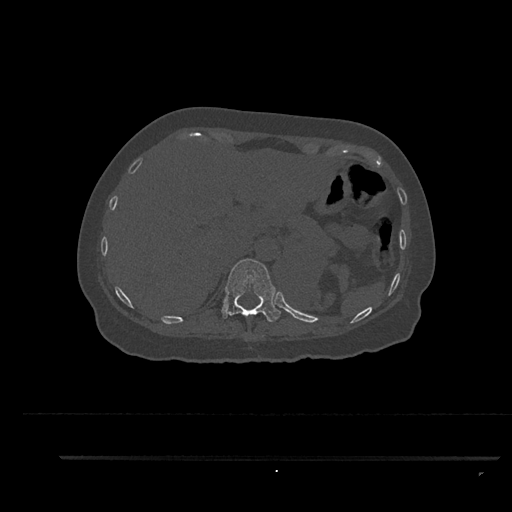
CT including the spine, one axial slice; position 320 of 797 along the scan axis; 120 kVp; bone window (W 1800 / L 400 HU); 0.5 mm slice thickness; 512 × 512 image matrix, field of view 408 × 408 mm. Patient: female, 44 years. From the clinical record (not read from this slice): primary cancer: renal.
Structures marked on this image (semi-automatically segmented with operator editing):
- T11 vertebra: bounding box (x1, y1, x2, y2) in pixels: (221, 258, 281, 322)